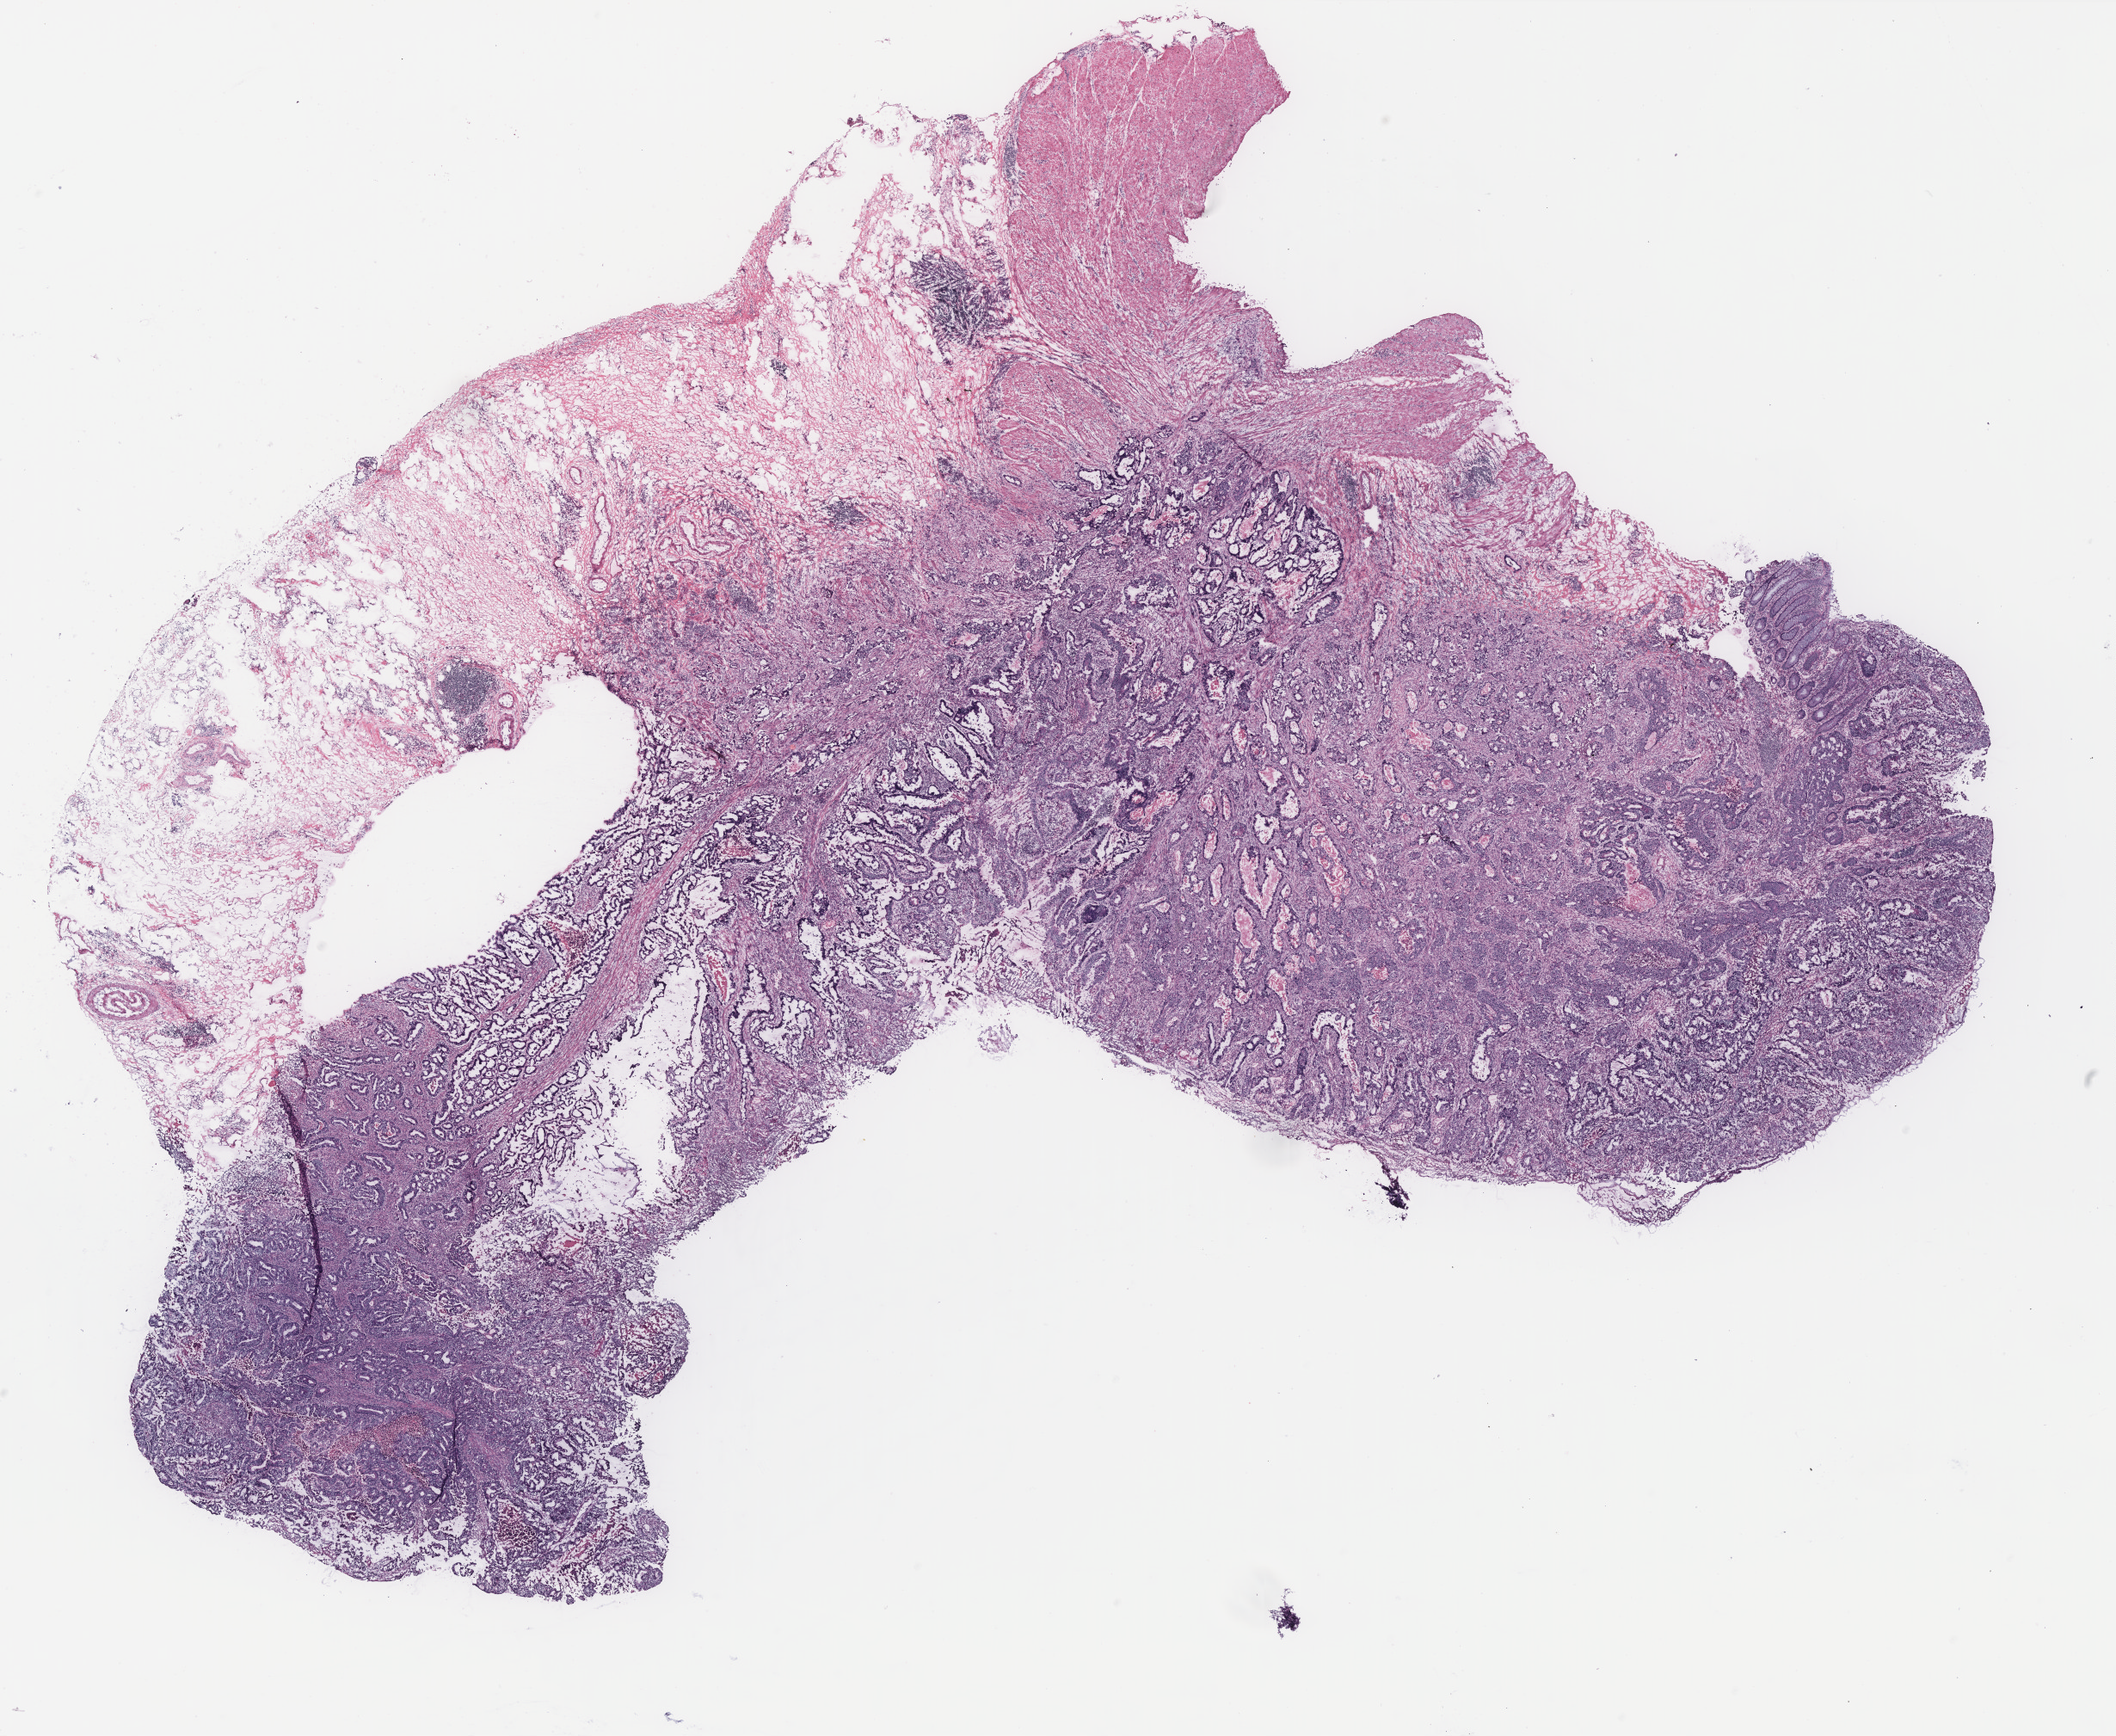
Digitized H&E-stained tissue section (whole slide), low-resolution overview of the scanned area, about 19.7 x 16.2 mm; colon, tissue type not recorded.
Patient diagnosis (cohort enrolment): colon cancer (colon).